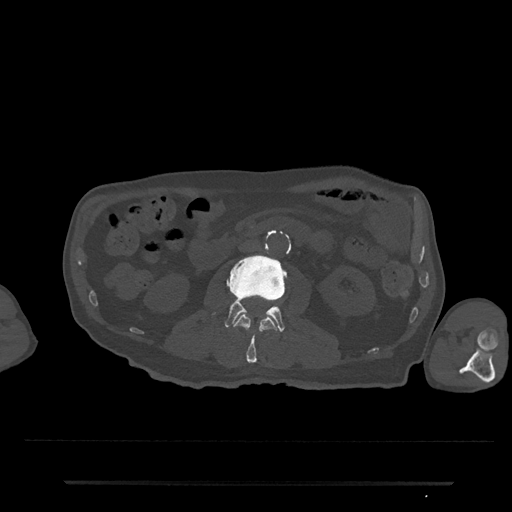
CT including the spine, one axial slice. Position 20 of 797 along the scan axis. 120 kVp. Bone window (W 1800 / L 400 HU). 512 × 512 image matrix, field of view 427 × 427 mm. Patient: male, 74 years. From the clinical record (not read from this slice): primary cancer: prostate.
Outlined on this slice (semi-automatically segmented with operator editing):
- L2 vertebra: bounding box (x1, y1, x2, y2) in pixels: (234, 314, 277, 364)
- L3 vertebra: (212, 255, 286, 332)